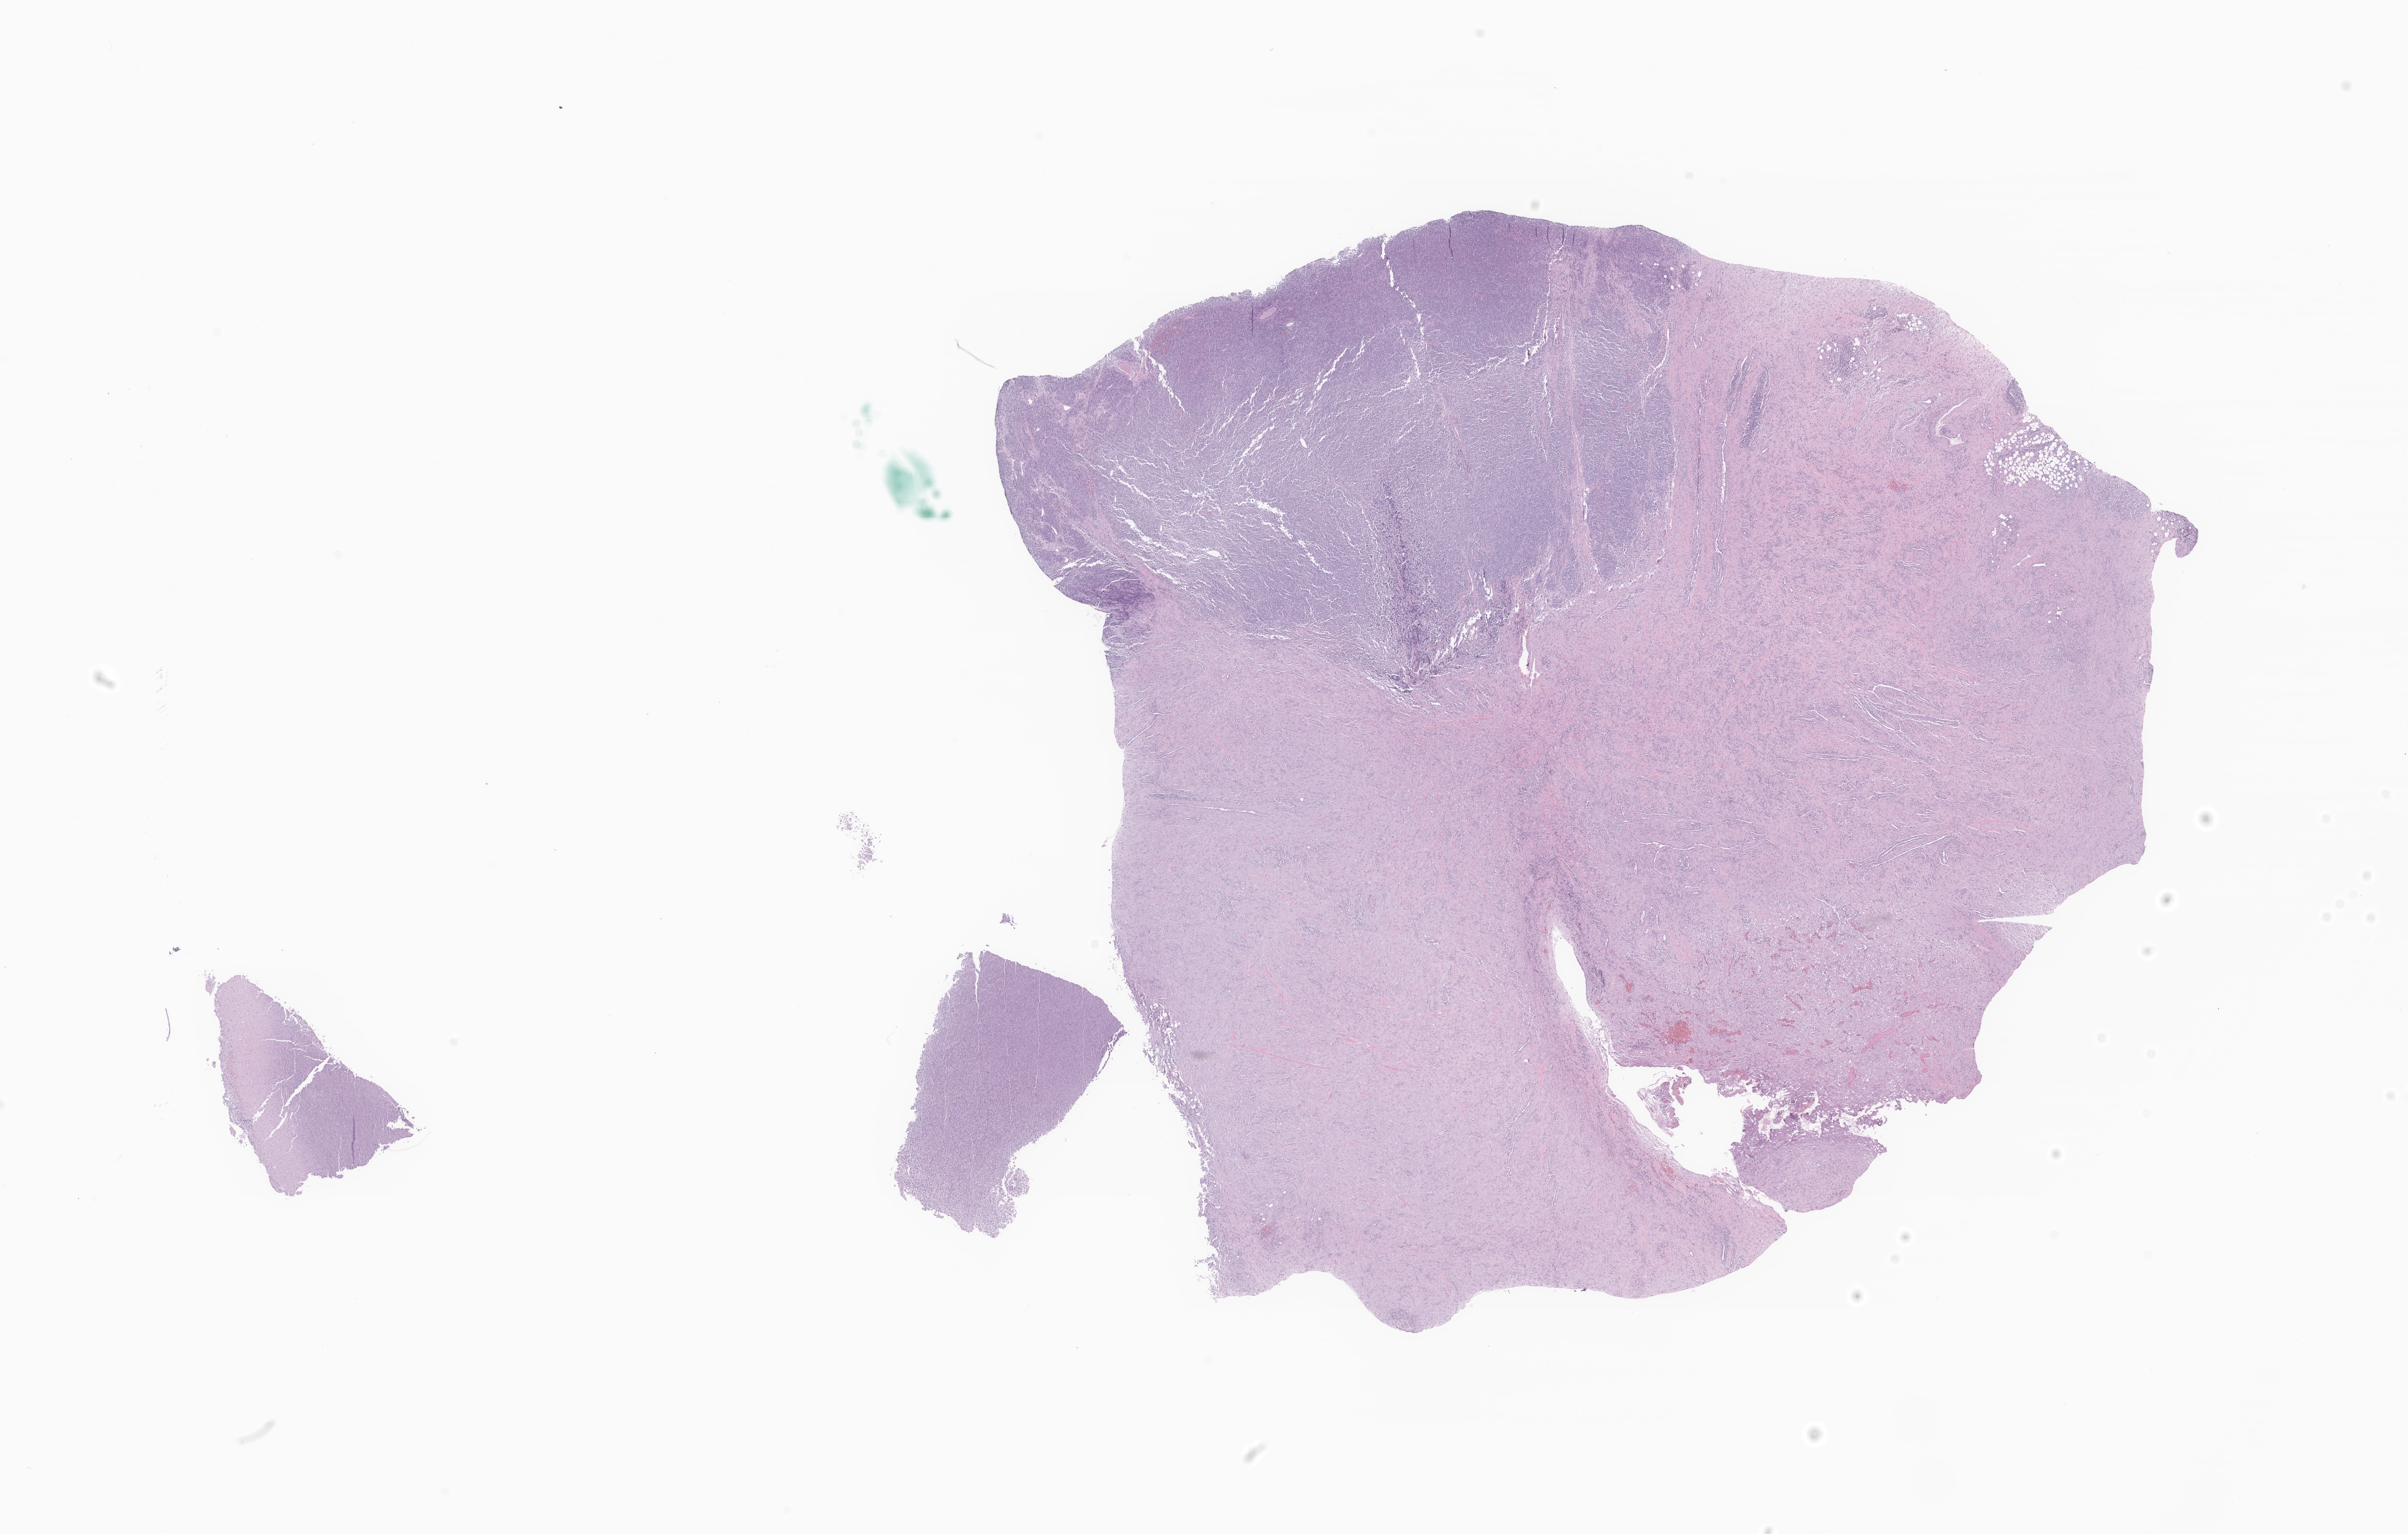
Haematoxylin and eosin whole-slide image of tumor tissue from the mediastinum, whole scanned area (about 22.7 x 14.5 mm) shown as a low-resolution overview; formalin-fixed, paraffin-embedded (FFPE) tissue. Patient: male, age 80 months (6 years 8 months).
Recorded diagnosis: Rhabdomyosarcoma, NOS.